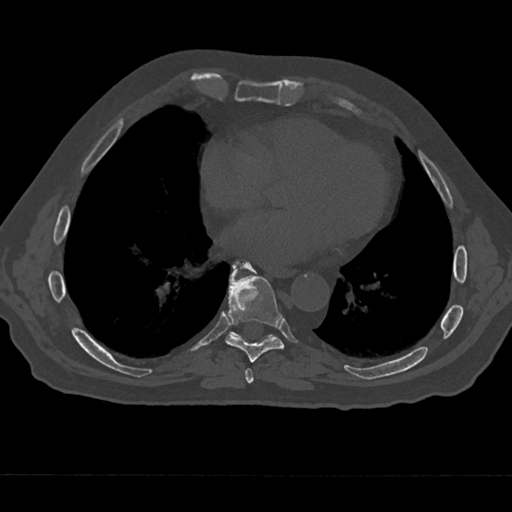
CT including the spine, one axial slice. Position 306 of 797 along the scan axis. Bone window (W 1800 / L 400 HU). 0.5 mm slice thickness. 512 × 512 image matrix. Male patient, age 75 years. Case-level facts recorded for this patient, not image findings: primary cancer: renal.
Outlined on this slice (semi-automatically segmented with operator editing):
- T7 vertebra: box from (x=239, y=367) to (x=258, y=385) px
- T8 vertebra: (x=225, y=261)–(x=285, y=362)
- T9 vertebra: (x=230, y=262)–(x=257, y=336)